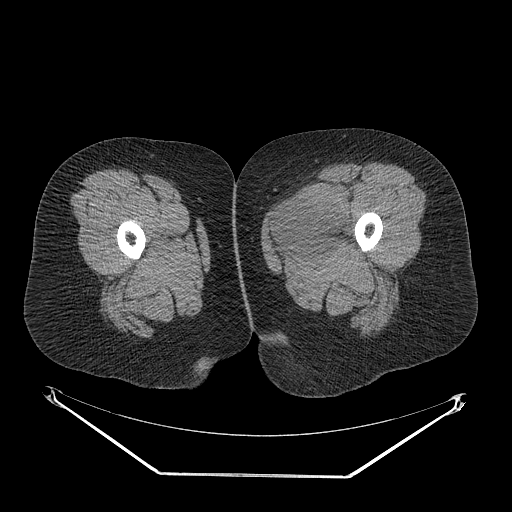
CT of an extremity soft-tissue mass (from a PET/CT study), one axial slice. Slice 20 of 267 in the series (ordered by position). Reconstruction kernel STANDARD. Soft-tissue window (W 400 / L 40 HU). 3.75 mm slice thickness. 512 × 512 image matrix. Female patient. From the clinical record (not read from this slice): histological type: myxofibrosarcoma; grade: intermediate; site of the primary tumour: left thigh.
Outlined on this slice (expert contour drawn on MRI and transferred to this co-registered scan by the dataset authors):
- gross tumour volume including surrounding oedema: bounding box [x1, y1, x2, y2] px = [270, 189, 352, 257]
- gross tumour volume (mass): [274, 192, 350, 257]